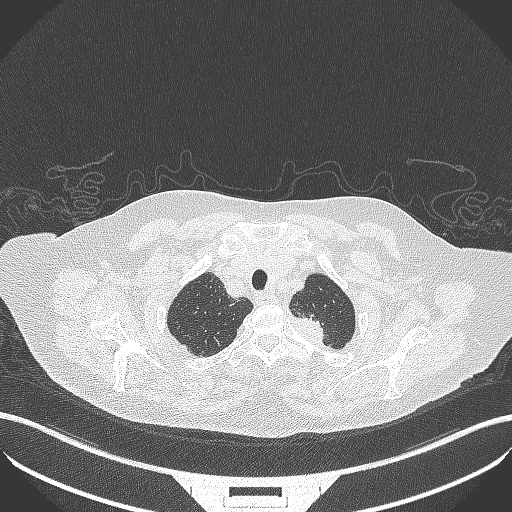
Chest CT, one axial slice. Reconstruction kernel B70f. 100 kVp. Lung window (W 1500 / L -600 HU). 512 × 512 image matrix, field of view 400 × 400 mm. Female patient, age 81 years. From the clinical record (not read from this slice): clinical TNM (as recorded): T2a N0 M0.
Outlined on this slice (bounding box drawn by a radiologist):
- lung tumour (recorded histology: adenocarcinoma): bounding box <287,313,336,350> (left, top, right, bottom; pixels)